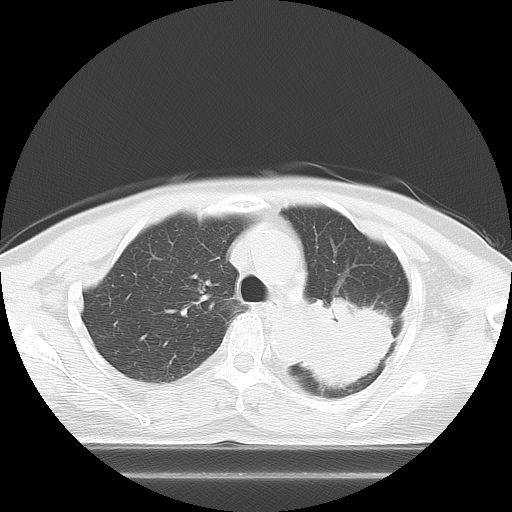
Chest CT, one axial slice. Position 6 of 21 along the scan axis. Reconstruction kernel LUNG. 120 kVp. Lung window (W 1500 / L -600 HU). 512 × 512 image matrix, field of view 350 × 350 mm. Female patient, age 74 years. Case-level facts recorded for this patient, not image findings: clinical TNM (as recorded): T3 N1 M1c; histopathological grade: G3.
Structures marked on this image (bounding box drawn by a radiologist):
- lung tumour (recorded histology: small cell carcinoma): bounding box [x1, y1, x2, y2] px = [293, 284, 401, 408]